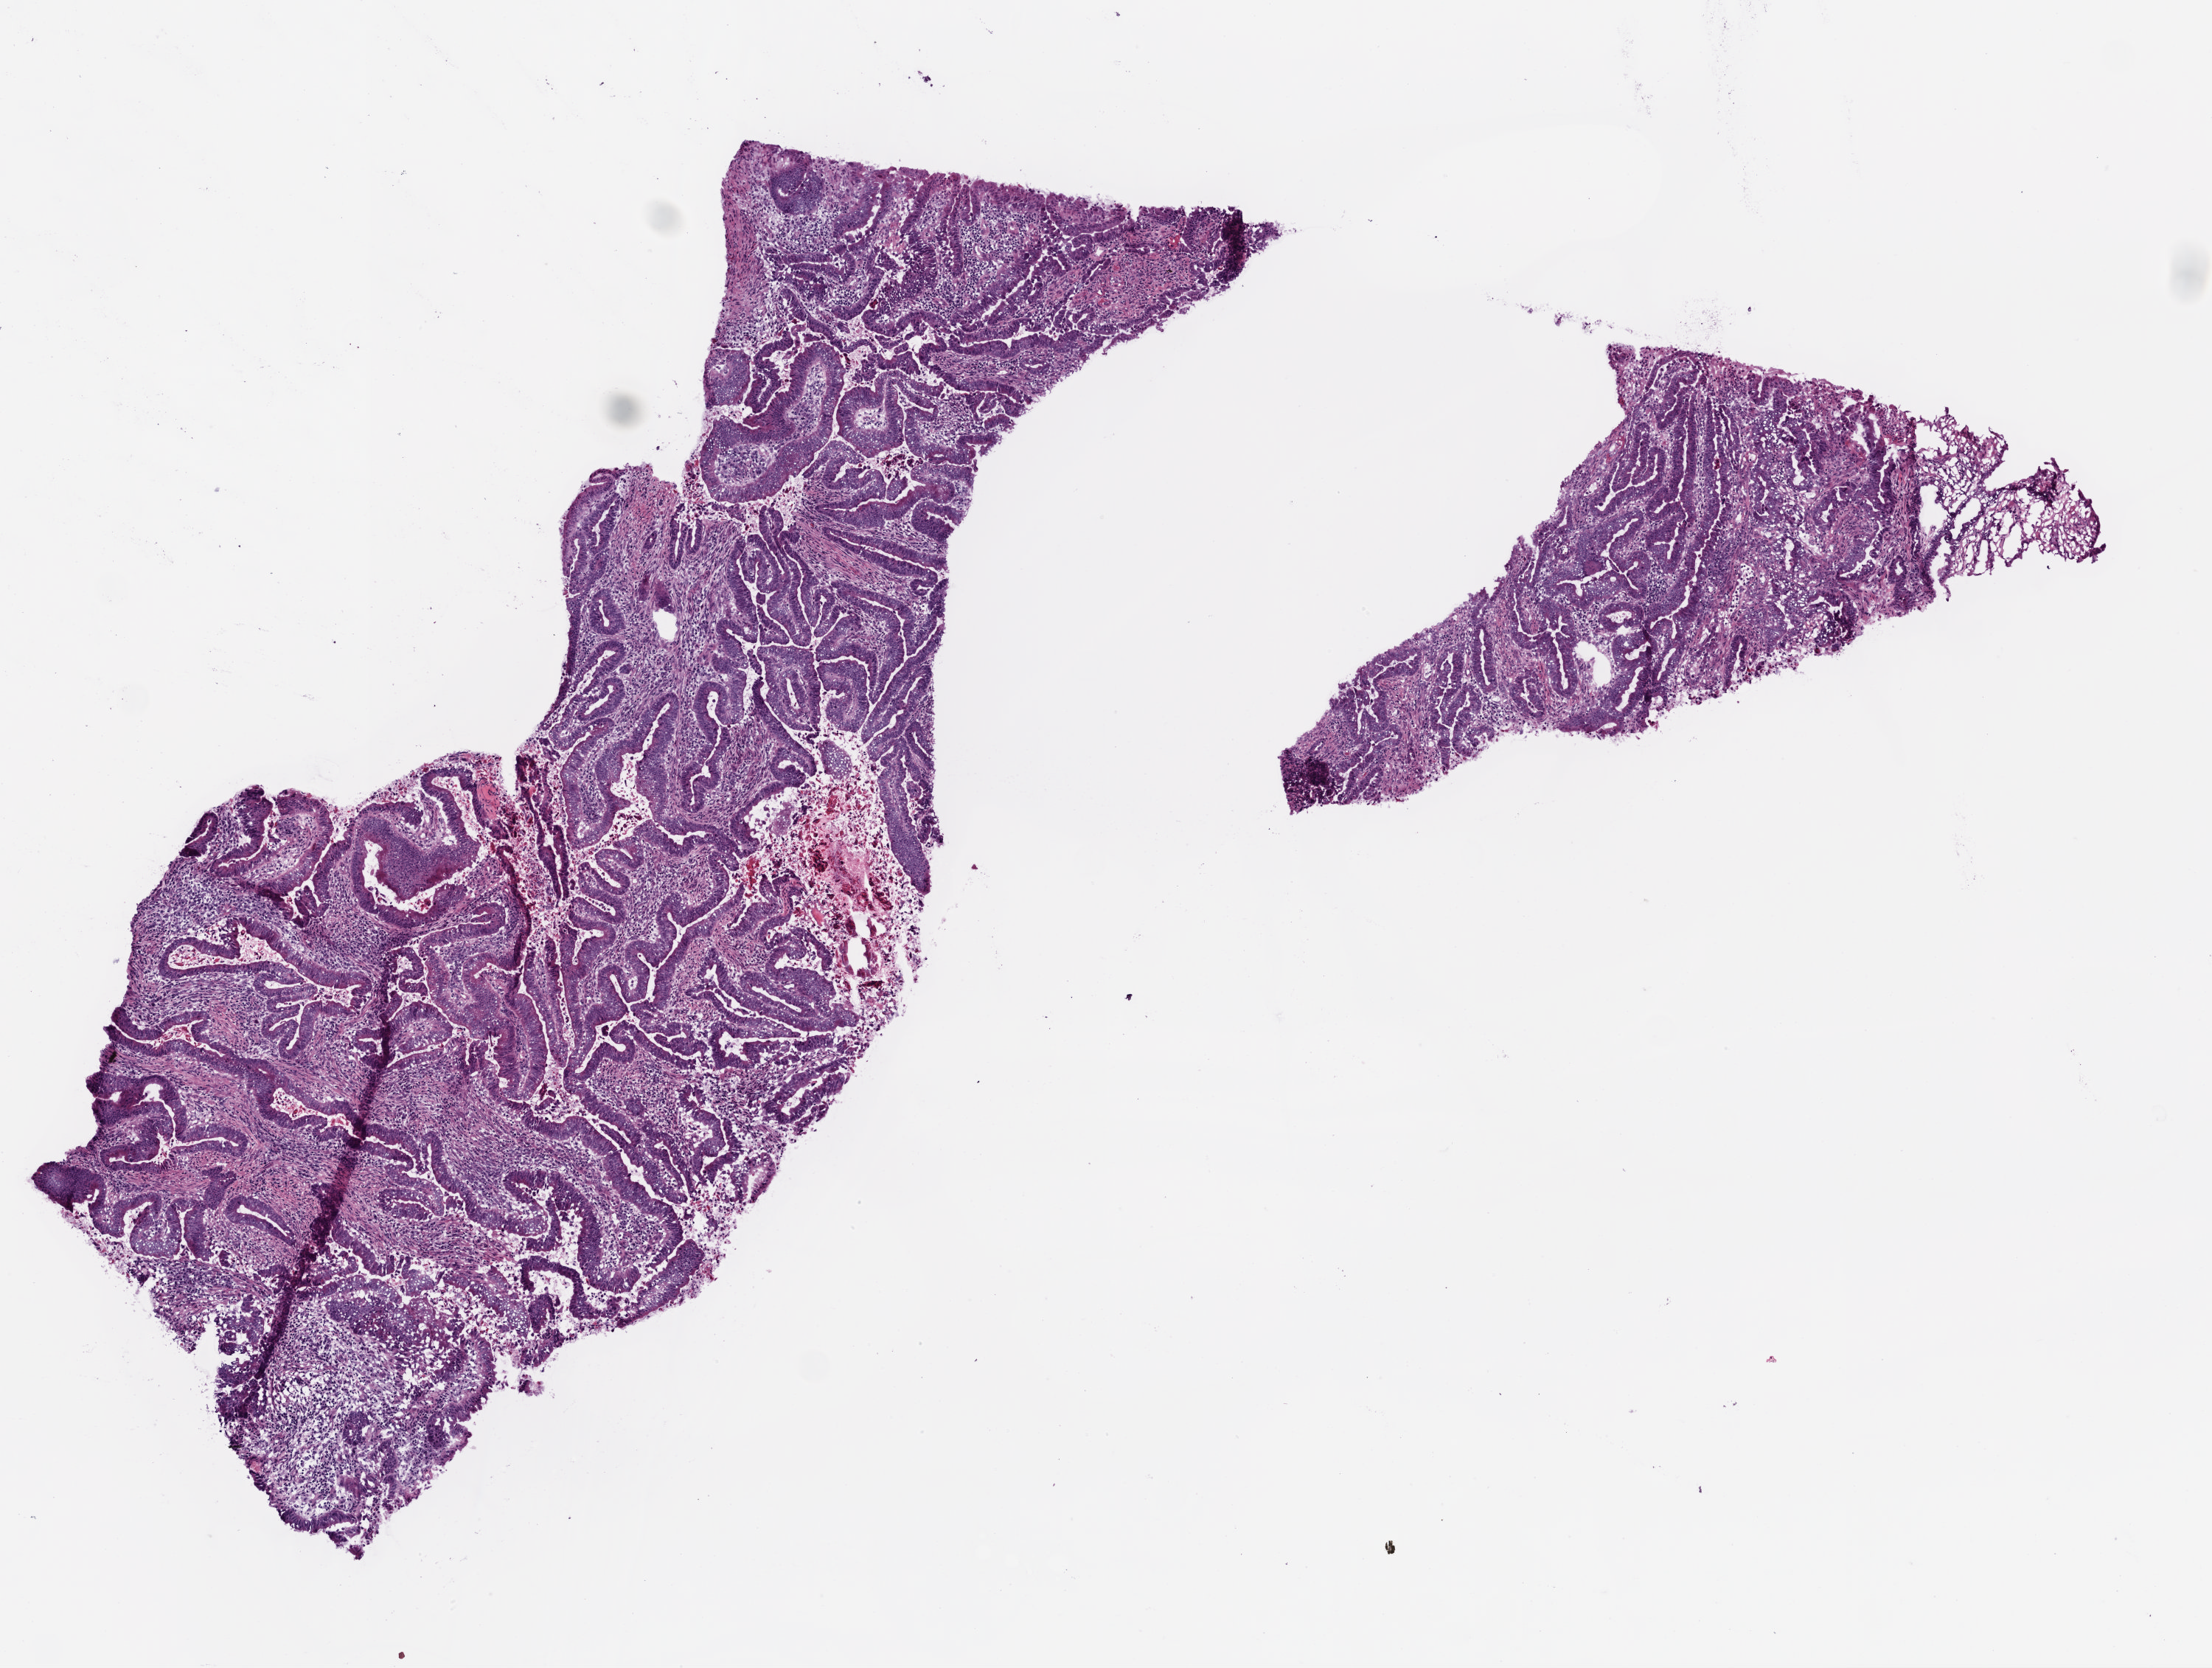
Digitized H&E-stained tissue section (whole slide) — whole scanned area (about 6.0 x 4.5 mm, from a 20x scan) shown as a low-resolution overview. Frozen section. Sample: primary tumour, colon. Female, age 80 years at initial diagnosis. Composition of this section per pathologist review: tumour cells 75%, tumour nuclei 70%, normal cells 0%, stromal cells 15%, necrosis 10%.
- AJCC pathologic stage: IIA (7th edition)
- TNM: T3 N0 M0
- lymph nodes positive (case pathology): 0 of 21 examined
- histologic diagnosis: Adenocarcinoma, NOS (sigmoid colon)